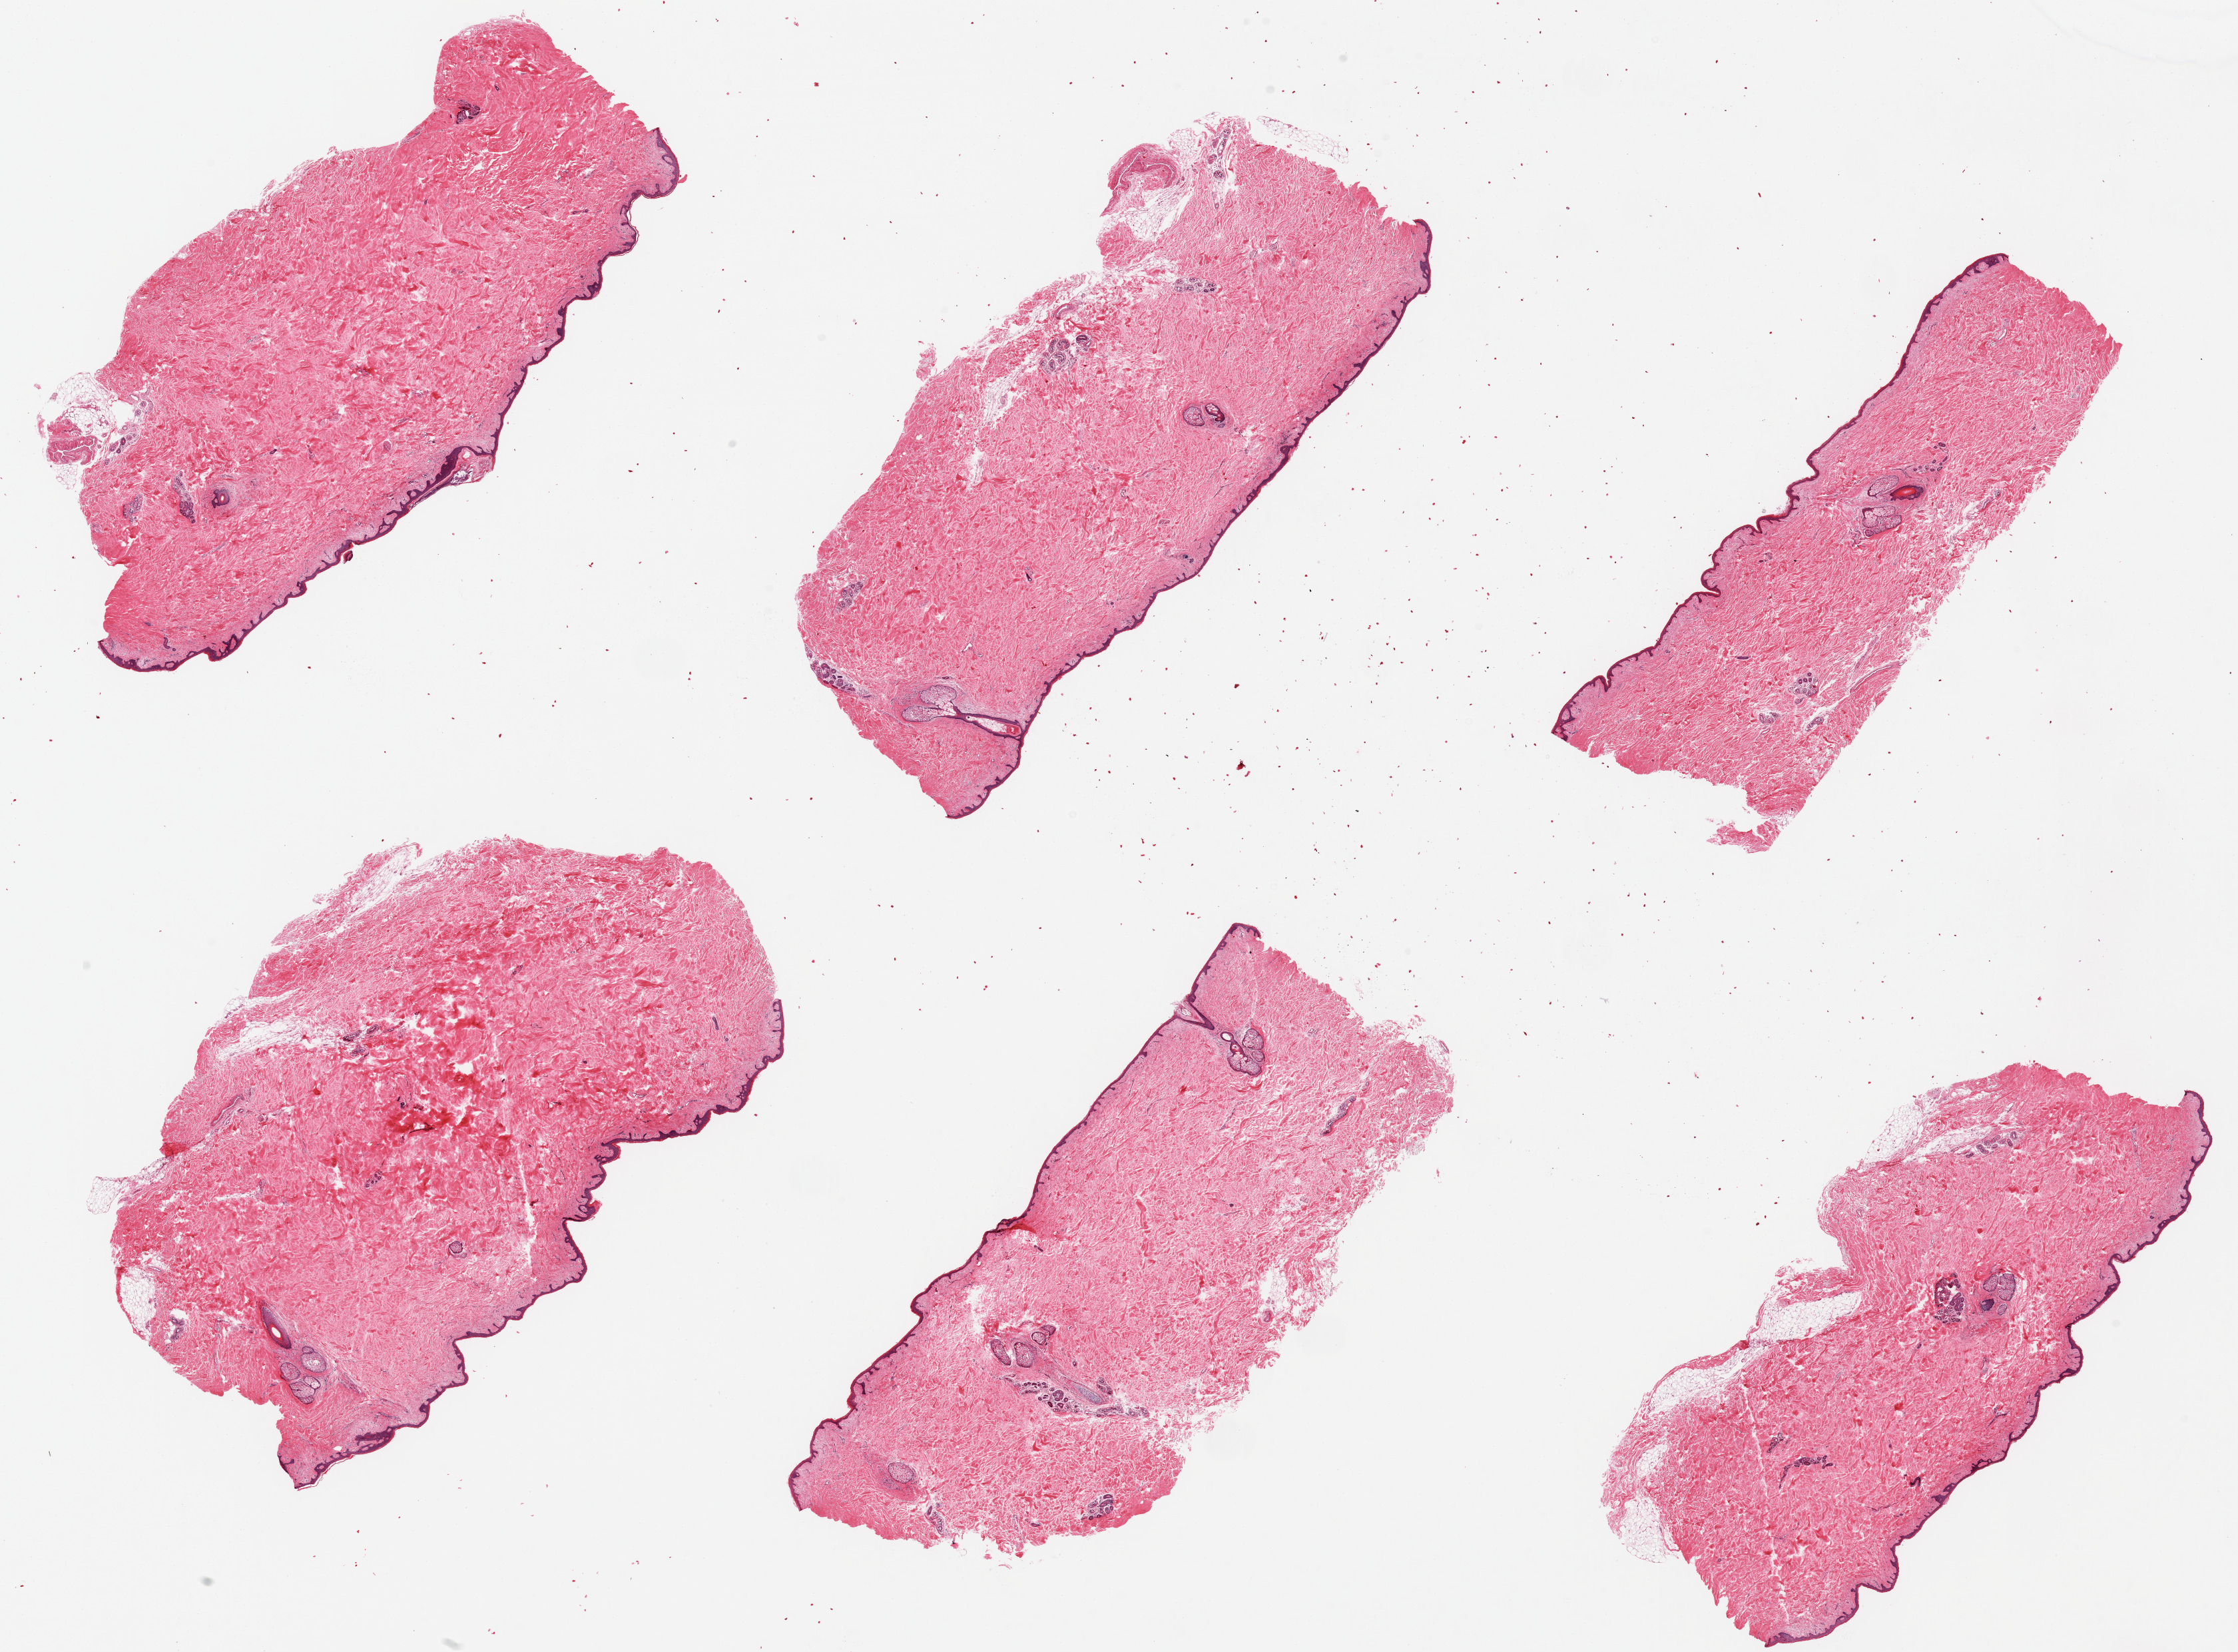
Digitized H&E-stained section, whole scanned area (about 26.6 x 19.6 mm) shown as a low-resolution overview; PAXgene-fixed, paraffin-embedded tissue; section of skin of suprapubic region (target tissue); donor tissue sample.
• reviewer comment on this tissue sample: 6 pieces; insignificant subcutaneous and periadnexal fat; epidermis ~34 micron thick